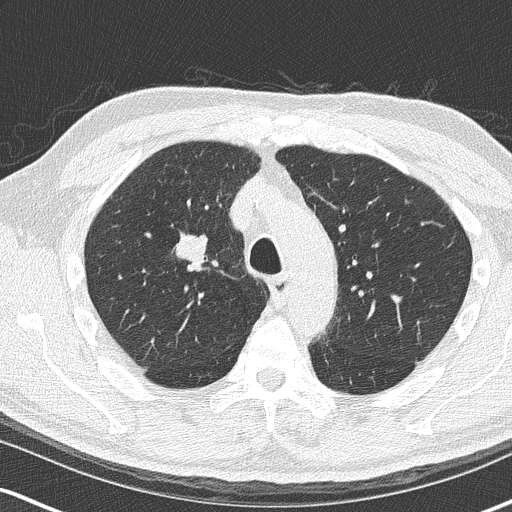
Chest CT (low-dose screening protocol), one axial image, second annual screen, lung window (W 1500 / L -600 HU), lung (sharp) reconstruction kernel (B50f), slice 59 of 170 in the series, 512 × 512 image matrix, field of view 320 × 320 mm. Male participant, aged 68 years at enrolment. Current smoker at enrolment.
Lesion marked by an expert reader, bounding box <152,225,217,288> (left, top, right, bottom; pixels). The exam's reader record, not a measurement of the box and not confirmed to be the same lesion: non-calcified nodule or mass ≥4 mm, right upper lobe, 18 × 15 mm, smooth margins, soft tissue attenuation, pre-existing on the prior screen: no. Later outcome: lung cancer diagnosed 136 days after this screen — small cell carcinoma, NOS, right upper lobe, stage IIIB (AJCC 6th edition), 20 mm at pathology.